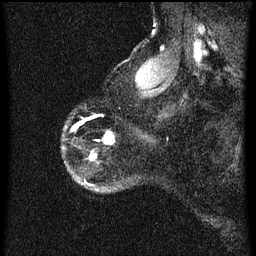
Breast MRI (dynamic contrast-enhanced), one sagittal slice; slice 54 of 60 in the series (ordered by position); dynamic contrast-enhanced series, image 2 of 3 at this slice position (ordered by acquisition); 1.5 T; TE 4.2 ms, TR 8 ms; 2 mm slice thickness; 256 × 256 image matrix, field of view 180 × 180 mm. Female patient, age 56 years.
Outlined on this slice (semi-automatic segmentation, software-assisted and operator-edited):
- analysis volume of interest (the breast-tissue region the enhancement analysis was run in; not a lesion): bounding box [x1, y1, x2, y2] px = [106, 136, 115, 145]
- tumour enhancement mask (voxels above the 70 % enhancement threshold inside the analysis volume of interest): [106, 136, 115, 145]